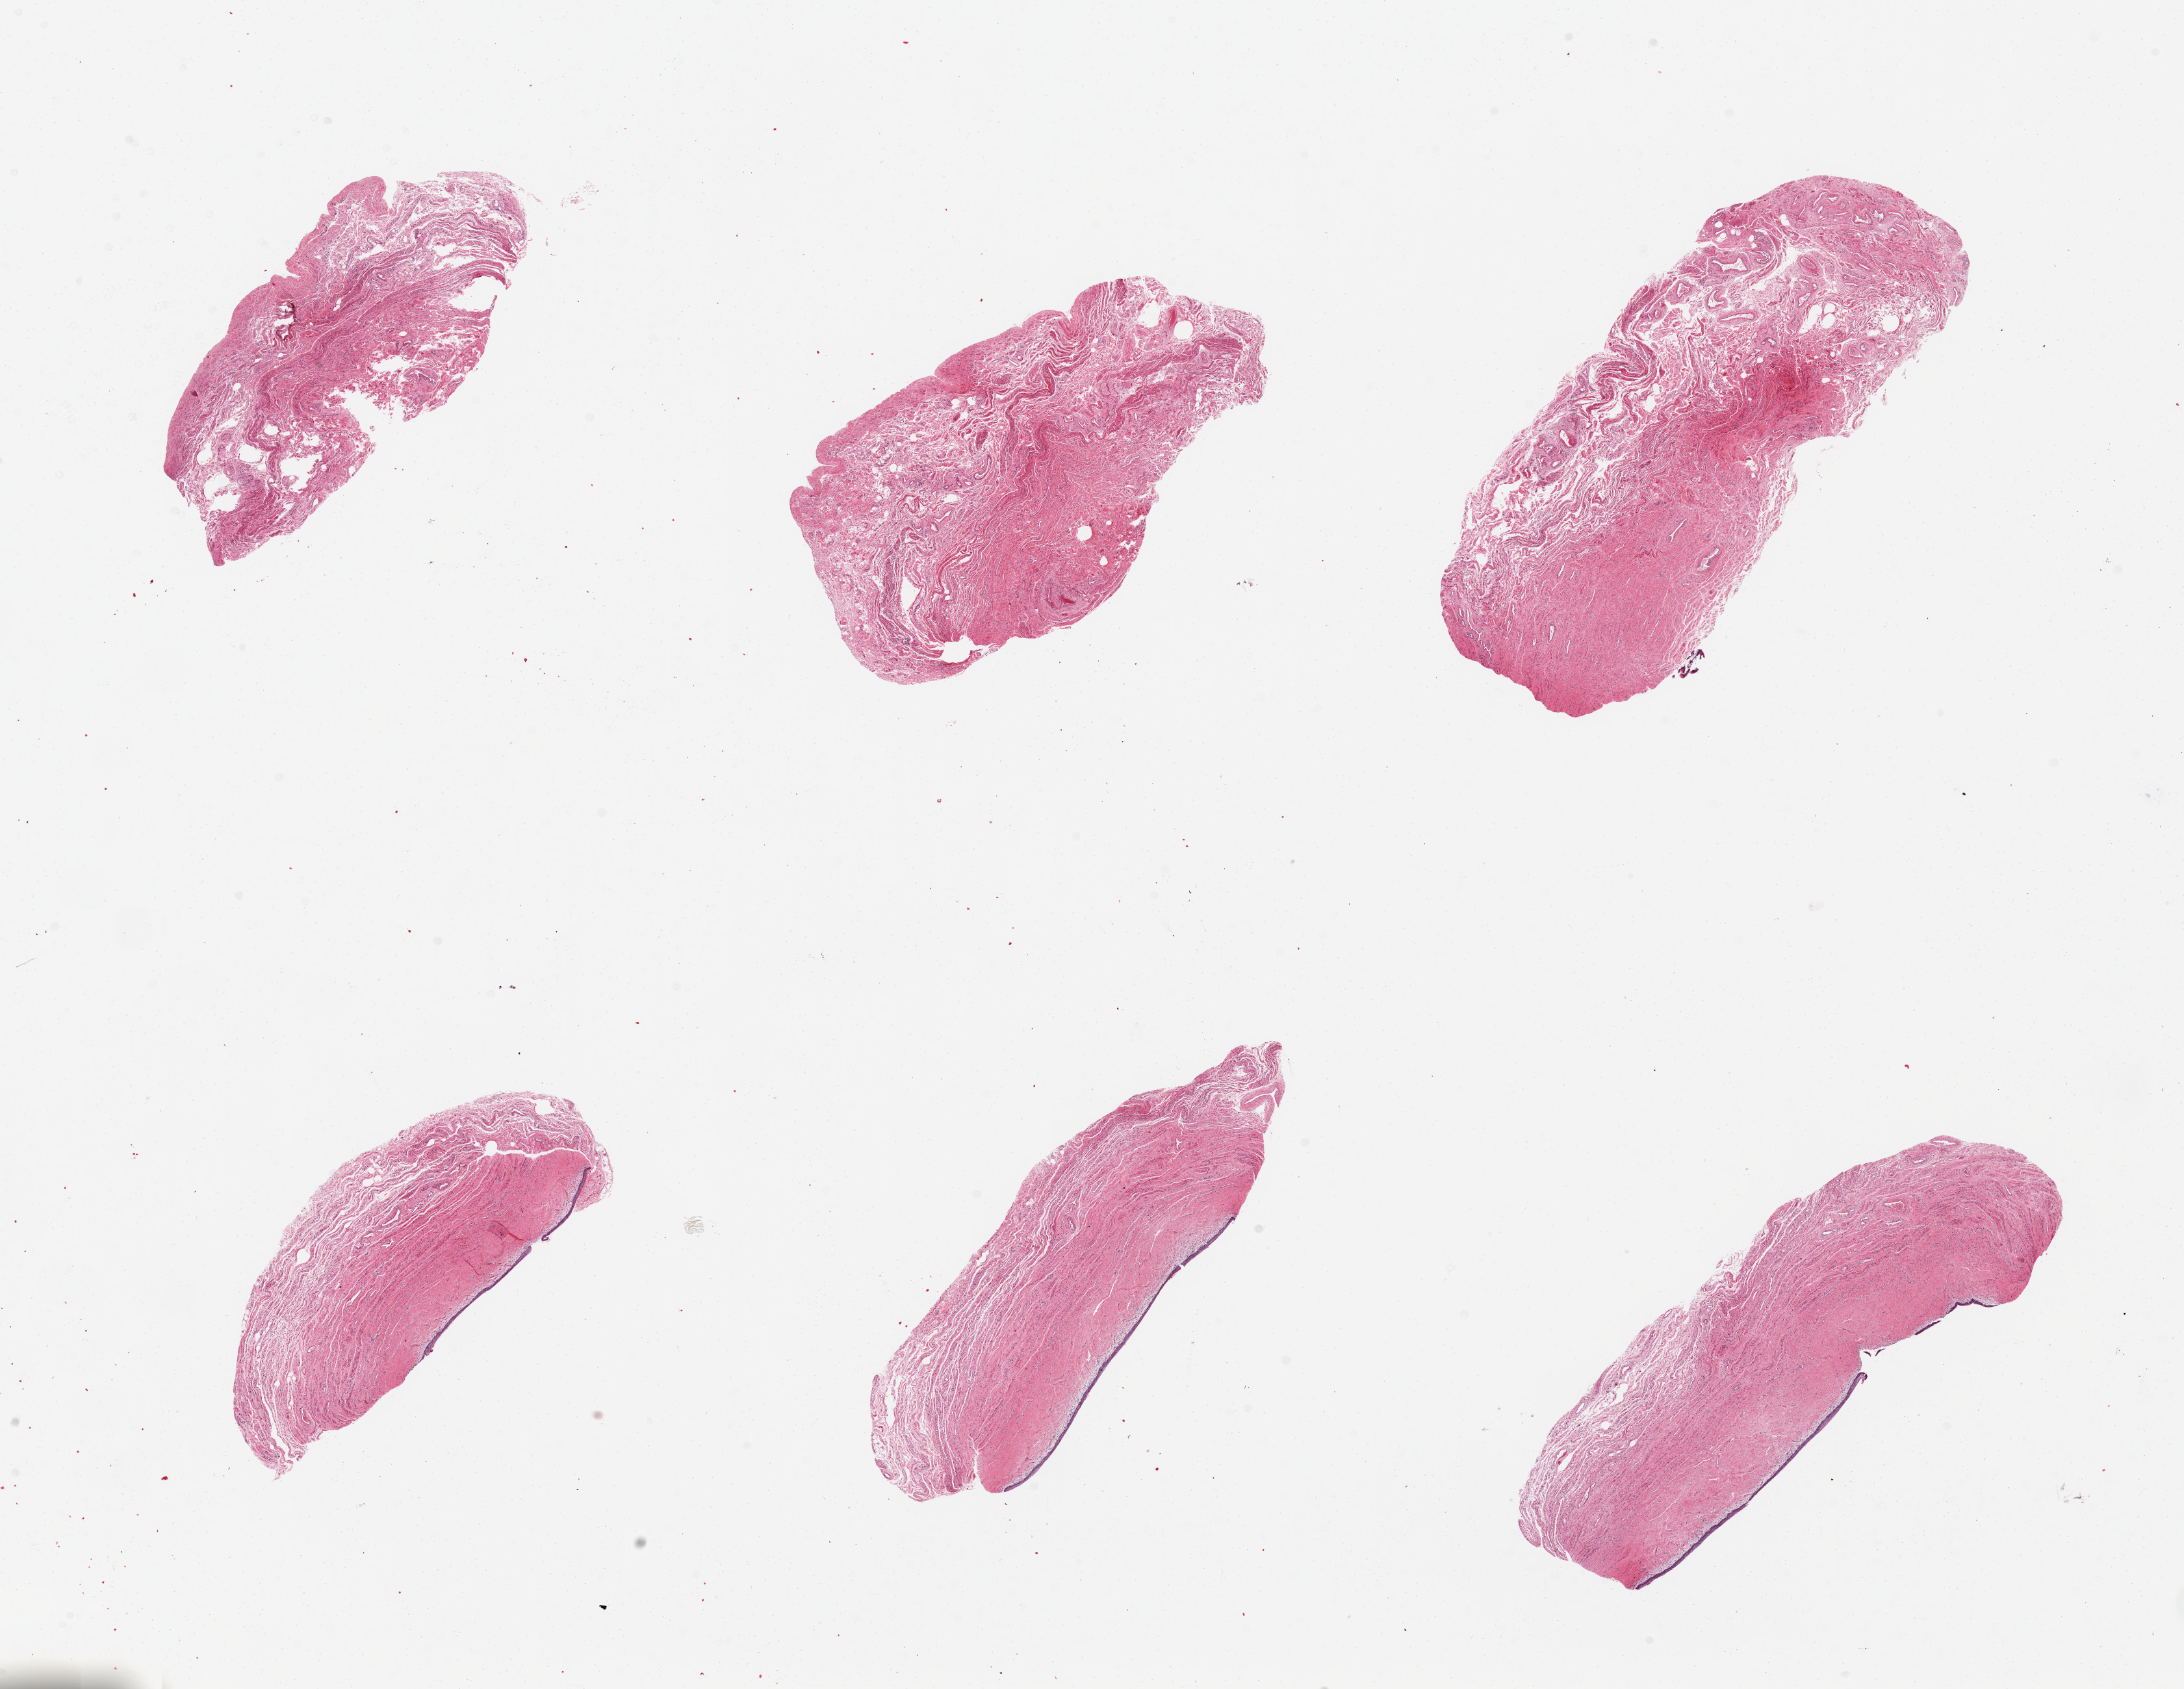
Digitized H&E-stained section — a low-resolution overview of the entire scanned area, about 26.6 x 20.6 mm (slide scanned at 20x), PAXgene-fixed, paraffin-embedded tissue, section of vagina (target tissue), tissue donor sample. Donor: female.
Reviewer comment on this tissue sample: 6 pieces, trace sloughing squamous mucosa on a few sections ~30 microns.